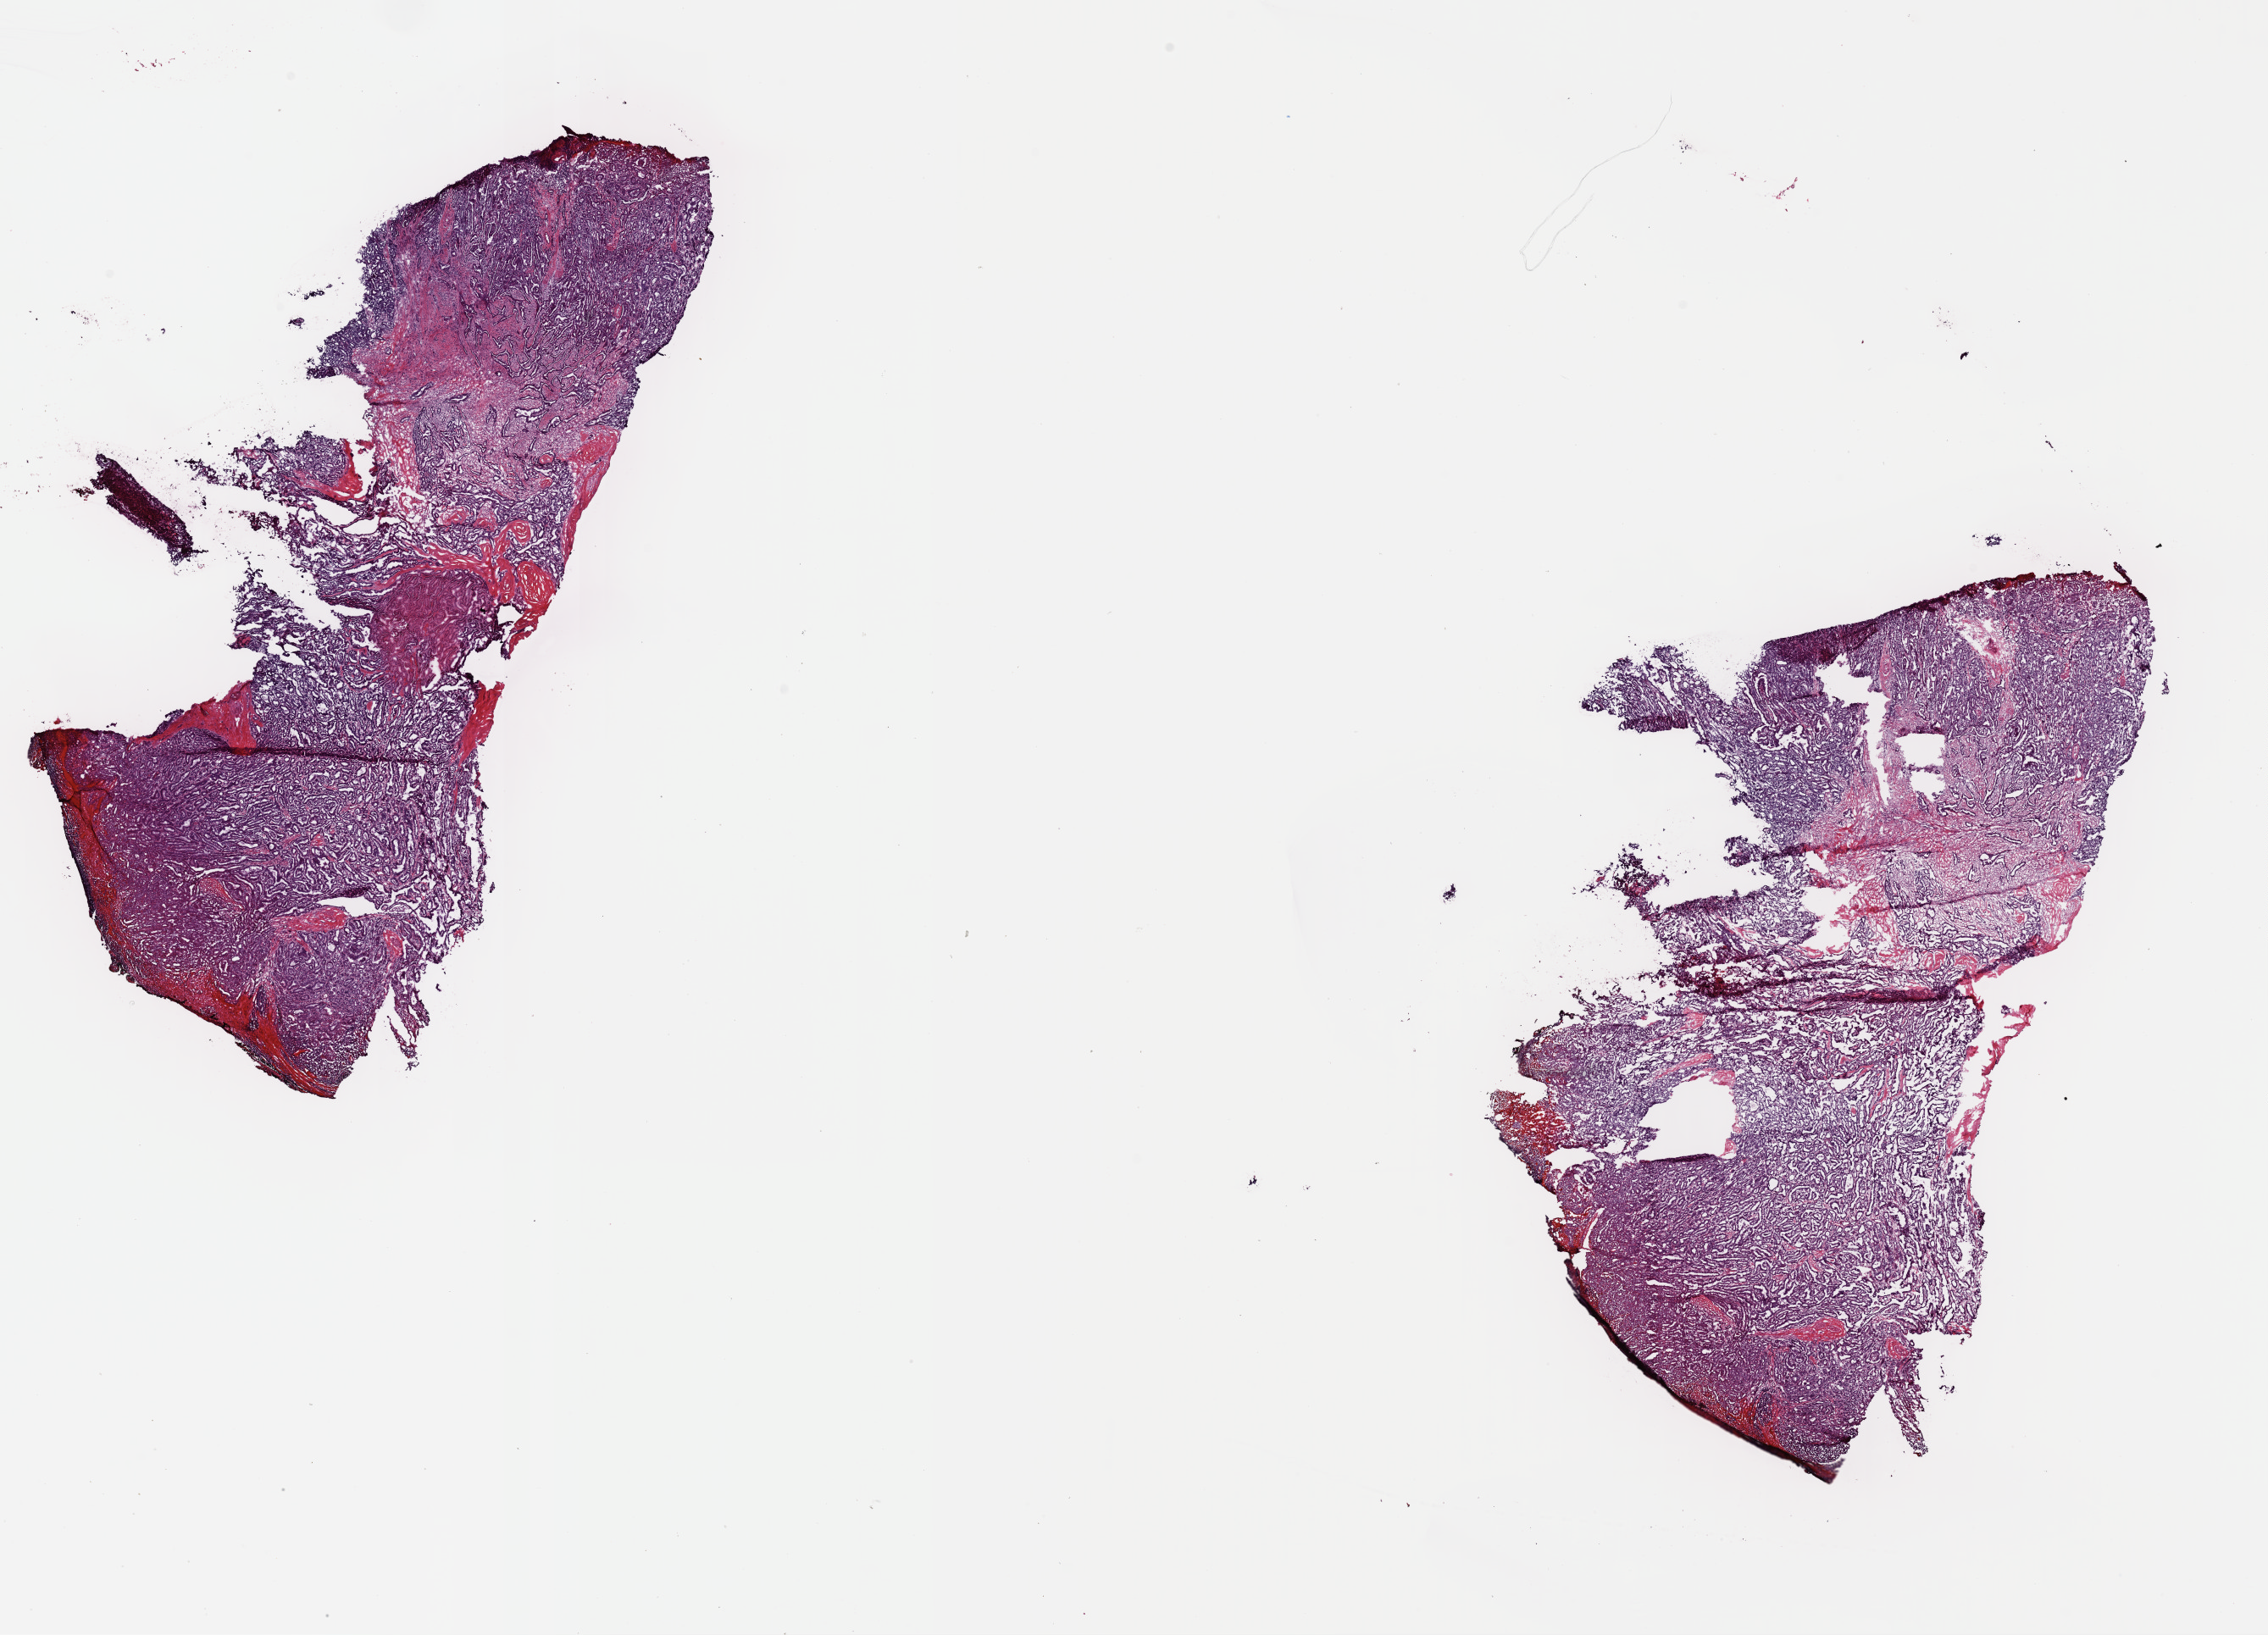
Digitized H&E-stained tissue section (whole slide) — low-resolution overview of the scanned area, about 21.1 x 15.2 mm (acquisition: 40x scan); frozen section; sample: primary tumour, thyroid. Female patient; age at initial diagnosis 44 years. Pathologist review of this section (percent, as recorded): tumour cells 90%, tumour nuclei 90%, normal cells 0%, stromal cells 10%, necrosis 0%. Inflammatory infiltration, as recorded: lymphocyte infiltration 1%, monocyte infiltration 1%, neutrophil infiltration 0%.
AJCC pathologic stage: I (7th edition). Lymph nodes positive (case pathology): 2 of 10 examined. Diagnosis: Papillary carcinoma, columnar cell (thyroid gland). Laterality: left.